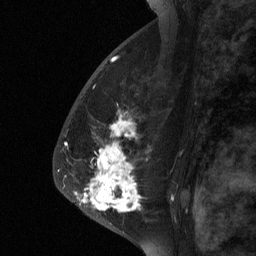
Breast MRI (dynamic contrast-enhanced), one sagittal slice. Position 41 of 64 along the scan axis. Dynamic contrast-enhanced study with each time point stored as its own series, time point 2 of 3 at this slice position (early post-contrast, ordered by acquisition time). 1.5 T. TE 4.8 ms, TR 27 ms. 2 mm slice thickness. 256 × 256 image matrix, field of view 180 × 180 mm. Patient: female, 56 years. From the clinical record (not read from this slice): setting: breast cancer imaged before/during neoadjuvant chemotherapy; receptor status: HER2-positive.
Outlined on this slice (semi-automatic segmentation, software-assisted and operator-edited):
- analysis volume of interest (the breast-tissue region the enhancement analysis was run in; not a lesion): bounding box (x1, y1, x2, y2) in pixels: (69, 104, 182, 229)
- tumour enhancement mask (voxels above the 90 % enhancement threshold inside the analysis volume of interest): (74, 123, 140, 212)